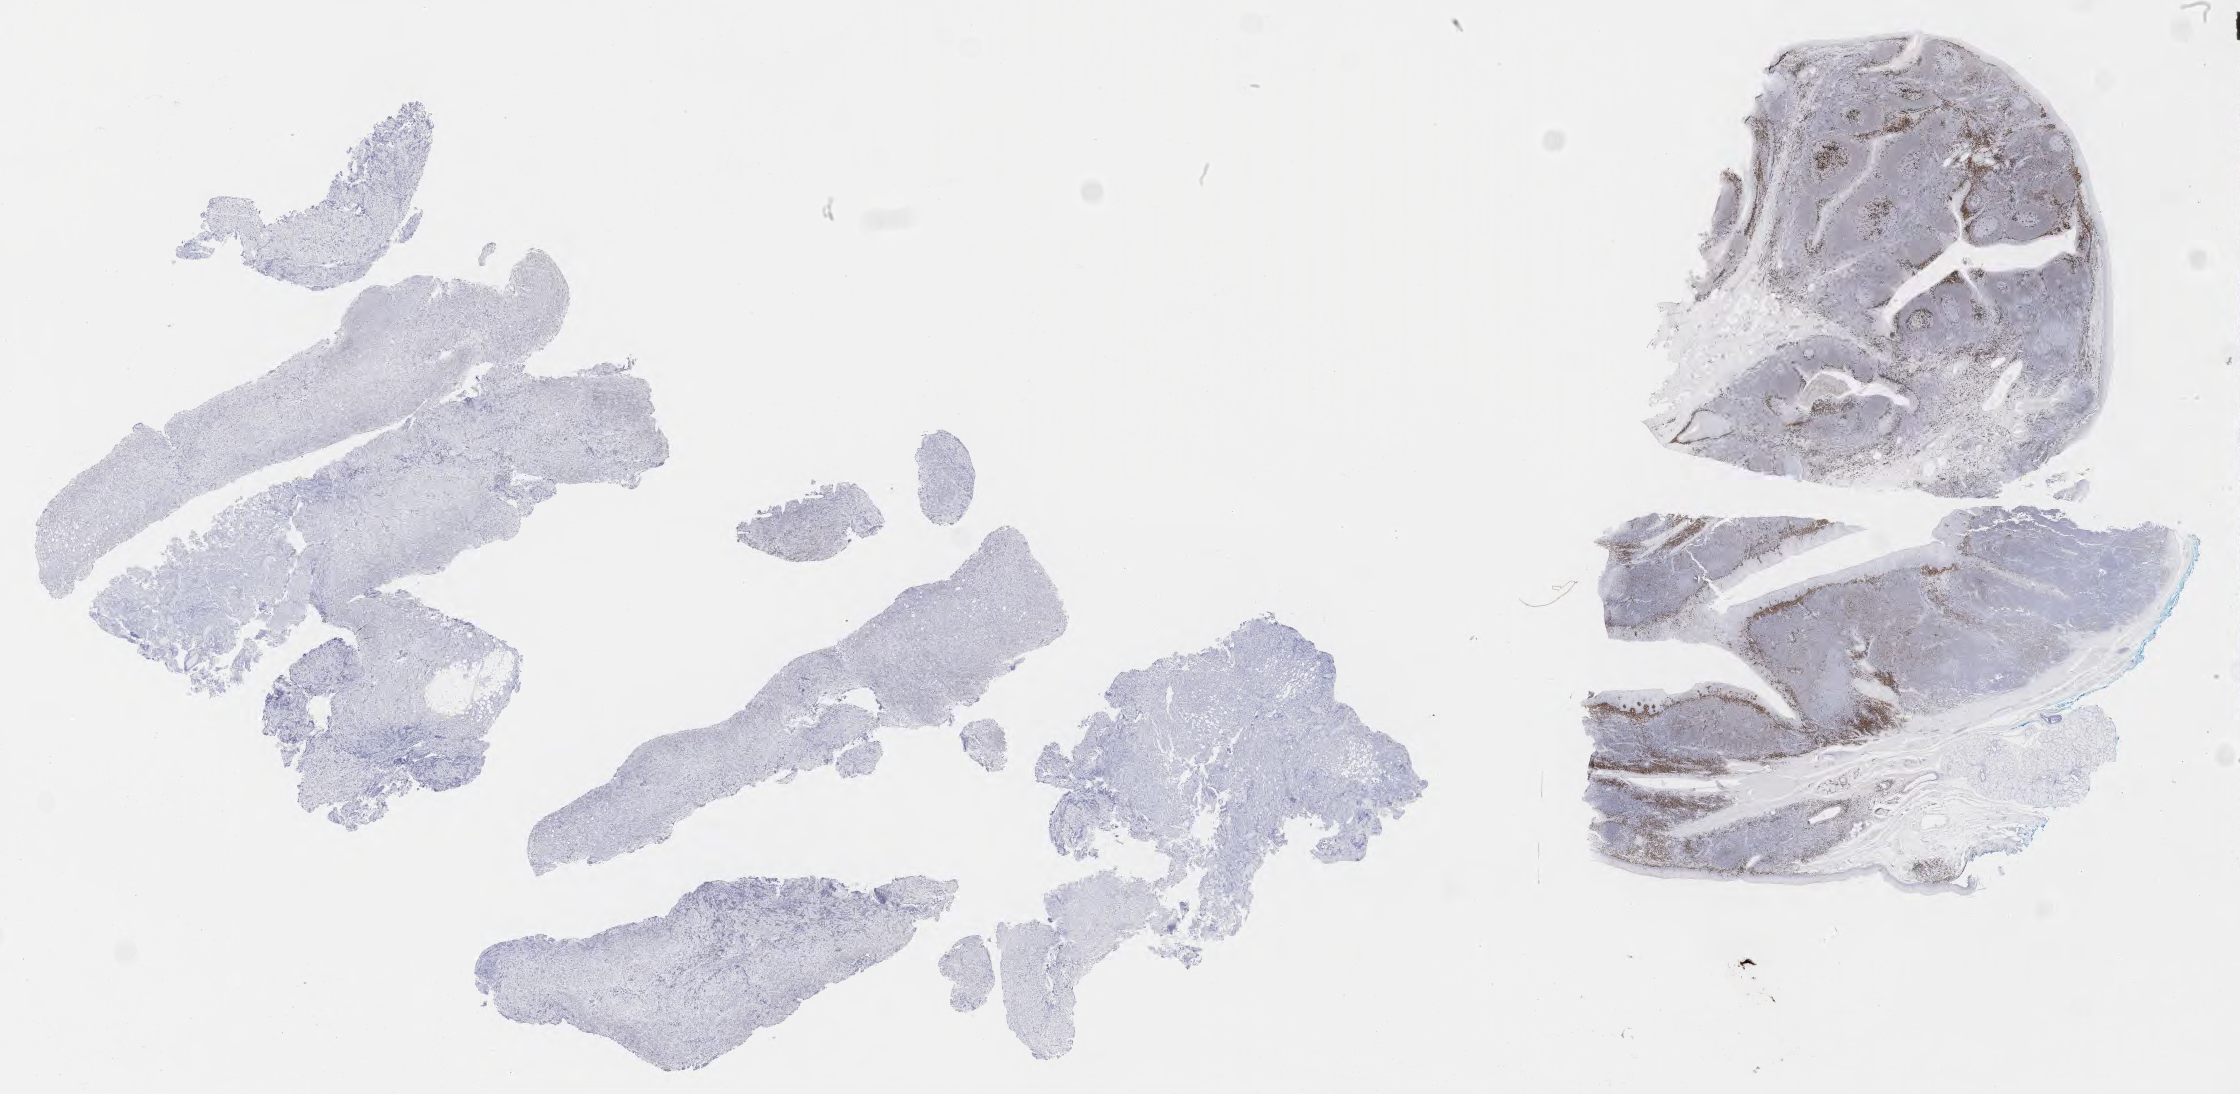
IHC for IRF4/MUM1, whole-slide image, low-resolution overview of the scanned area, about 36.2 x 17.7 mm. Tumor tissue. Patient male; age 45 years.
* diagnosis: Diffuse large B-cell lymphoma, NOS